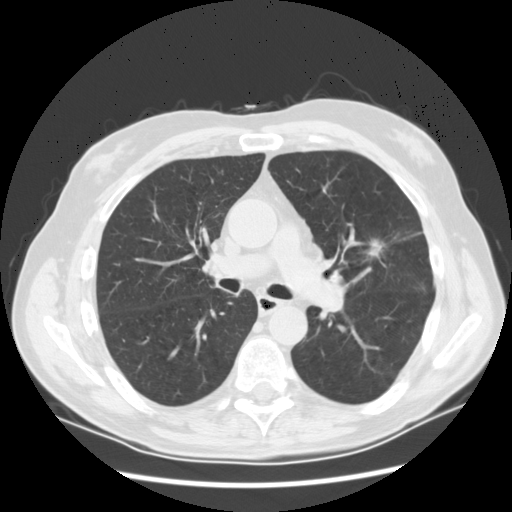
Axial slice from a low-dose chest CT screening exam; first (baseline) screen; lung window (W 1500 / L -600 HU); standard (soft-tissue) reconstruction kernel (STANDARD); 120 kVp. Male participant, aged 65 years at enrolment. Current smoker at enrolment.
Expert-annotated lung lesion, bounding box [x1, y1, x2, y2] px = [350, 224, 416, 292]. Screening reader's record for this exam (one nodule recorded; not confirmed to be the boxed lesion): non-calcified nodule or mass ≥4 mm, left upper lobe, 37 × 27 mm, spiculated (stellate) margins, soft tissue attenuation. Participant outcome: lung cancer diagnosed 56 days after this screen — non-small cell carcinoma, poorly differentiated (G3), stage IA (AJCC 6th edition).